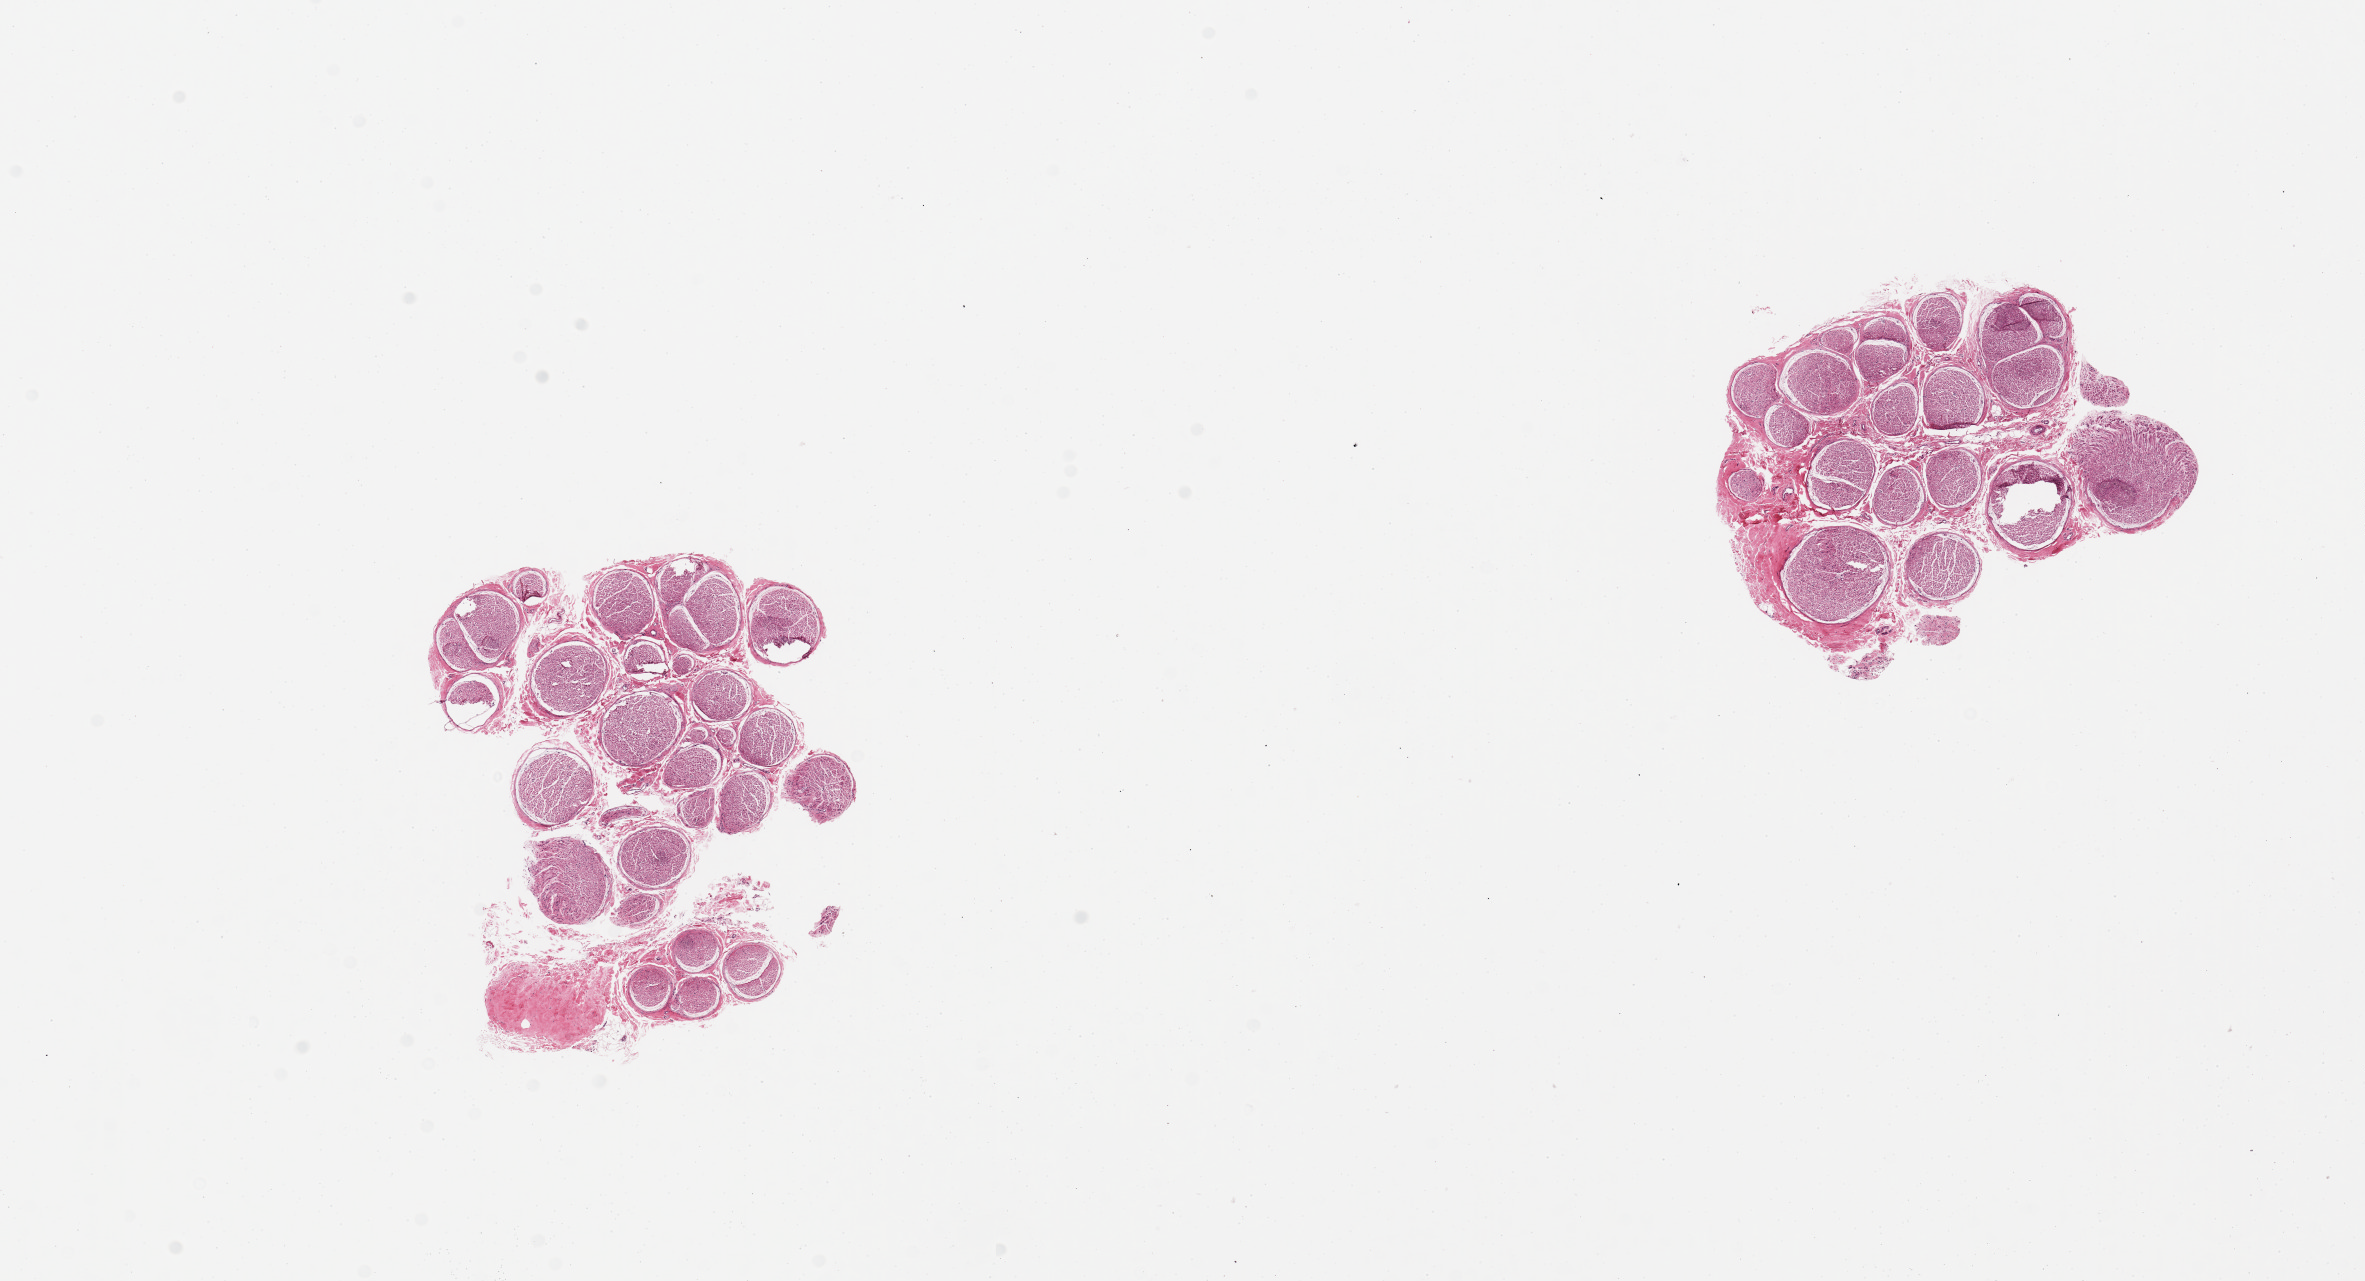
Whole-slide image, hematoxylin and eosin (H&E) stain, brightfield — low-resolution overview of the scanned area, about 18.7 x 10.1 mm (from a 20x scan). PAXgene-fixed paraffin-embedded (PFPE) section. Sampled site (target tissue): tibial nerve. Donor tissue sample.
- review note (as recorded): 2 pieces, 4x3 & 4x3mm. Well trimmed of adipose